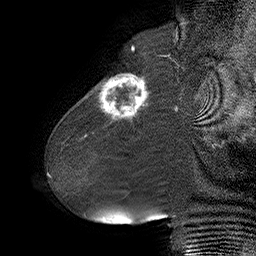
Breast MRI (dynamic contrast-enhanced), one sagittal slice. Slice 16 of 55 in the series (ordered by position). Dynamic contrast-enhanced series, time point 2 of 6 at this slice position (early post-contrast). 1.5 T. TE 4.5 ms, TR 32.4 ms. 256 × 256 image matrix, field of view 180 × 180 mm. Female patient. Case-level facts recorded for this patient, not image findings: setting: breast cancer imaged before/during neoadjuvant chemotherapy; receptor status: HER2-positive.
Structures marked on this image (semi-automatic segmentation, software-assisted and operator-edited):
- analysis volume of interest (the breast-tissue region the enhancement analysis was run in; not a lesion): box from (x=80, y=64) to (x=163, y=134) px
- tumour enhancement mask (voxels above the 100 % enhancement threshold inside the analysis volume of interest): (x=99, y=74)–(x=148, y=122)